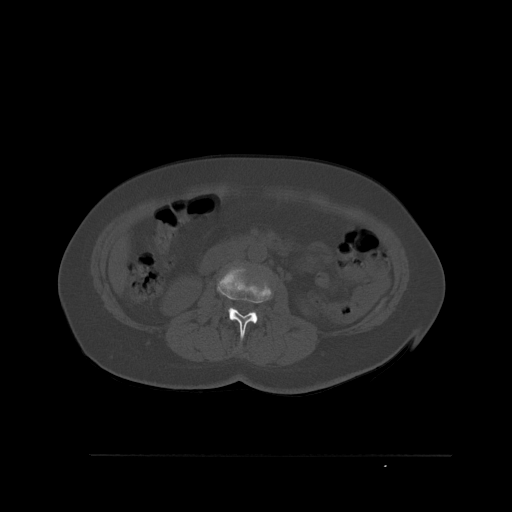
CT including the spine, one axial slice. Slice 242 of 527 in the series (ordered by position). Bone window (W 1800 / L 400 HU). 1.5 mm slice thickness. 512 × 512 image matrix. Patient: female, 73 years. From the clinical record (not read from this slice): primary cancer: breast; vertebrae with lytic lesions (as recorded): L2.
Outlined on this slice (semi-automatic segmentation, software-assisted and operator-edited):
- L2 vertebra: bounding box [x1, y1, x2, y2] px = [221, 265, 270, 340]
- L3 vertebra: [222, 274, 229, 314]